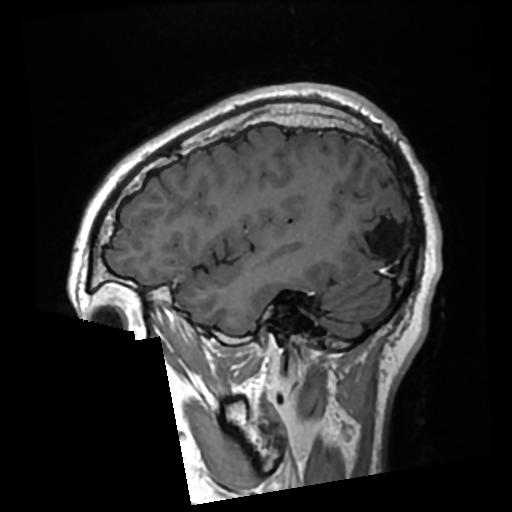
Brain MRI from a brain-tumour surgery series, one sagittal slice; slice 79 of 276 in the series (ordered by position); T1-weighted post-contrast; 0.7 mm slice thickness; 512 × 512 image matrix. From the clinical record (not read from this slice): histopathology: Glioma with ependymal features; WHO grade: 2; tumour location: Left Parietal.
Annotated regions visible in this slice (expert manual segmentation):
- previous resection cavity: bounding box [x1, y1, x2, y2] px = [354, 218, 400, 261]